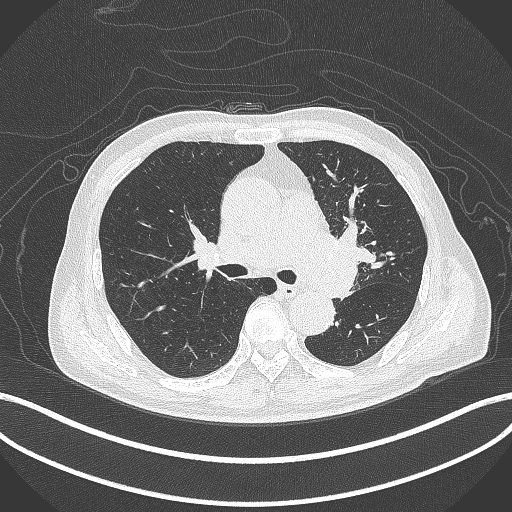
Chest CT, one axial slice. Position 265 of 417 along the scan axis. Reconstruction kernel B70f. 120 kVp. Lung window (W 1500 / L -600 HU). 1 mm slice thickness. 512 × 512 image matrix, field of view 400 × 400 mm. Male patient, age 77 years. From the clinical record (not read from this slice): clinical TNM (as recorded): T3 N1 M0.
Outlined on this slice (bounding box drawn by a radiologist):
- lung tumour (recorded histology: adenocarcinoma): bounding box [x1, y1, x2, y2] px = [306, 227, 369, 301]